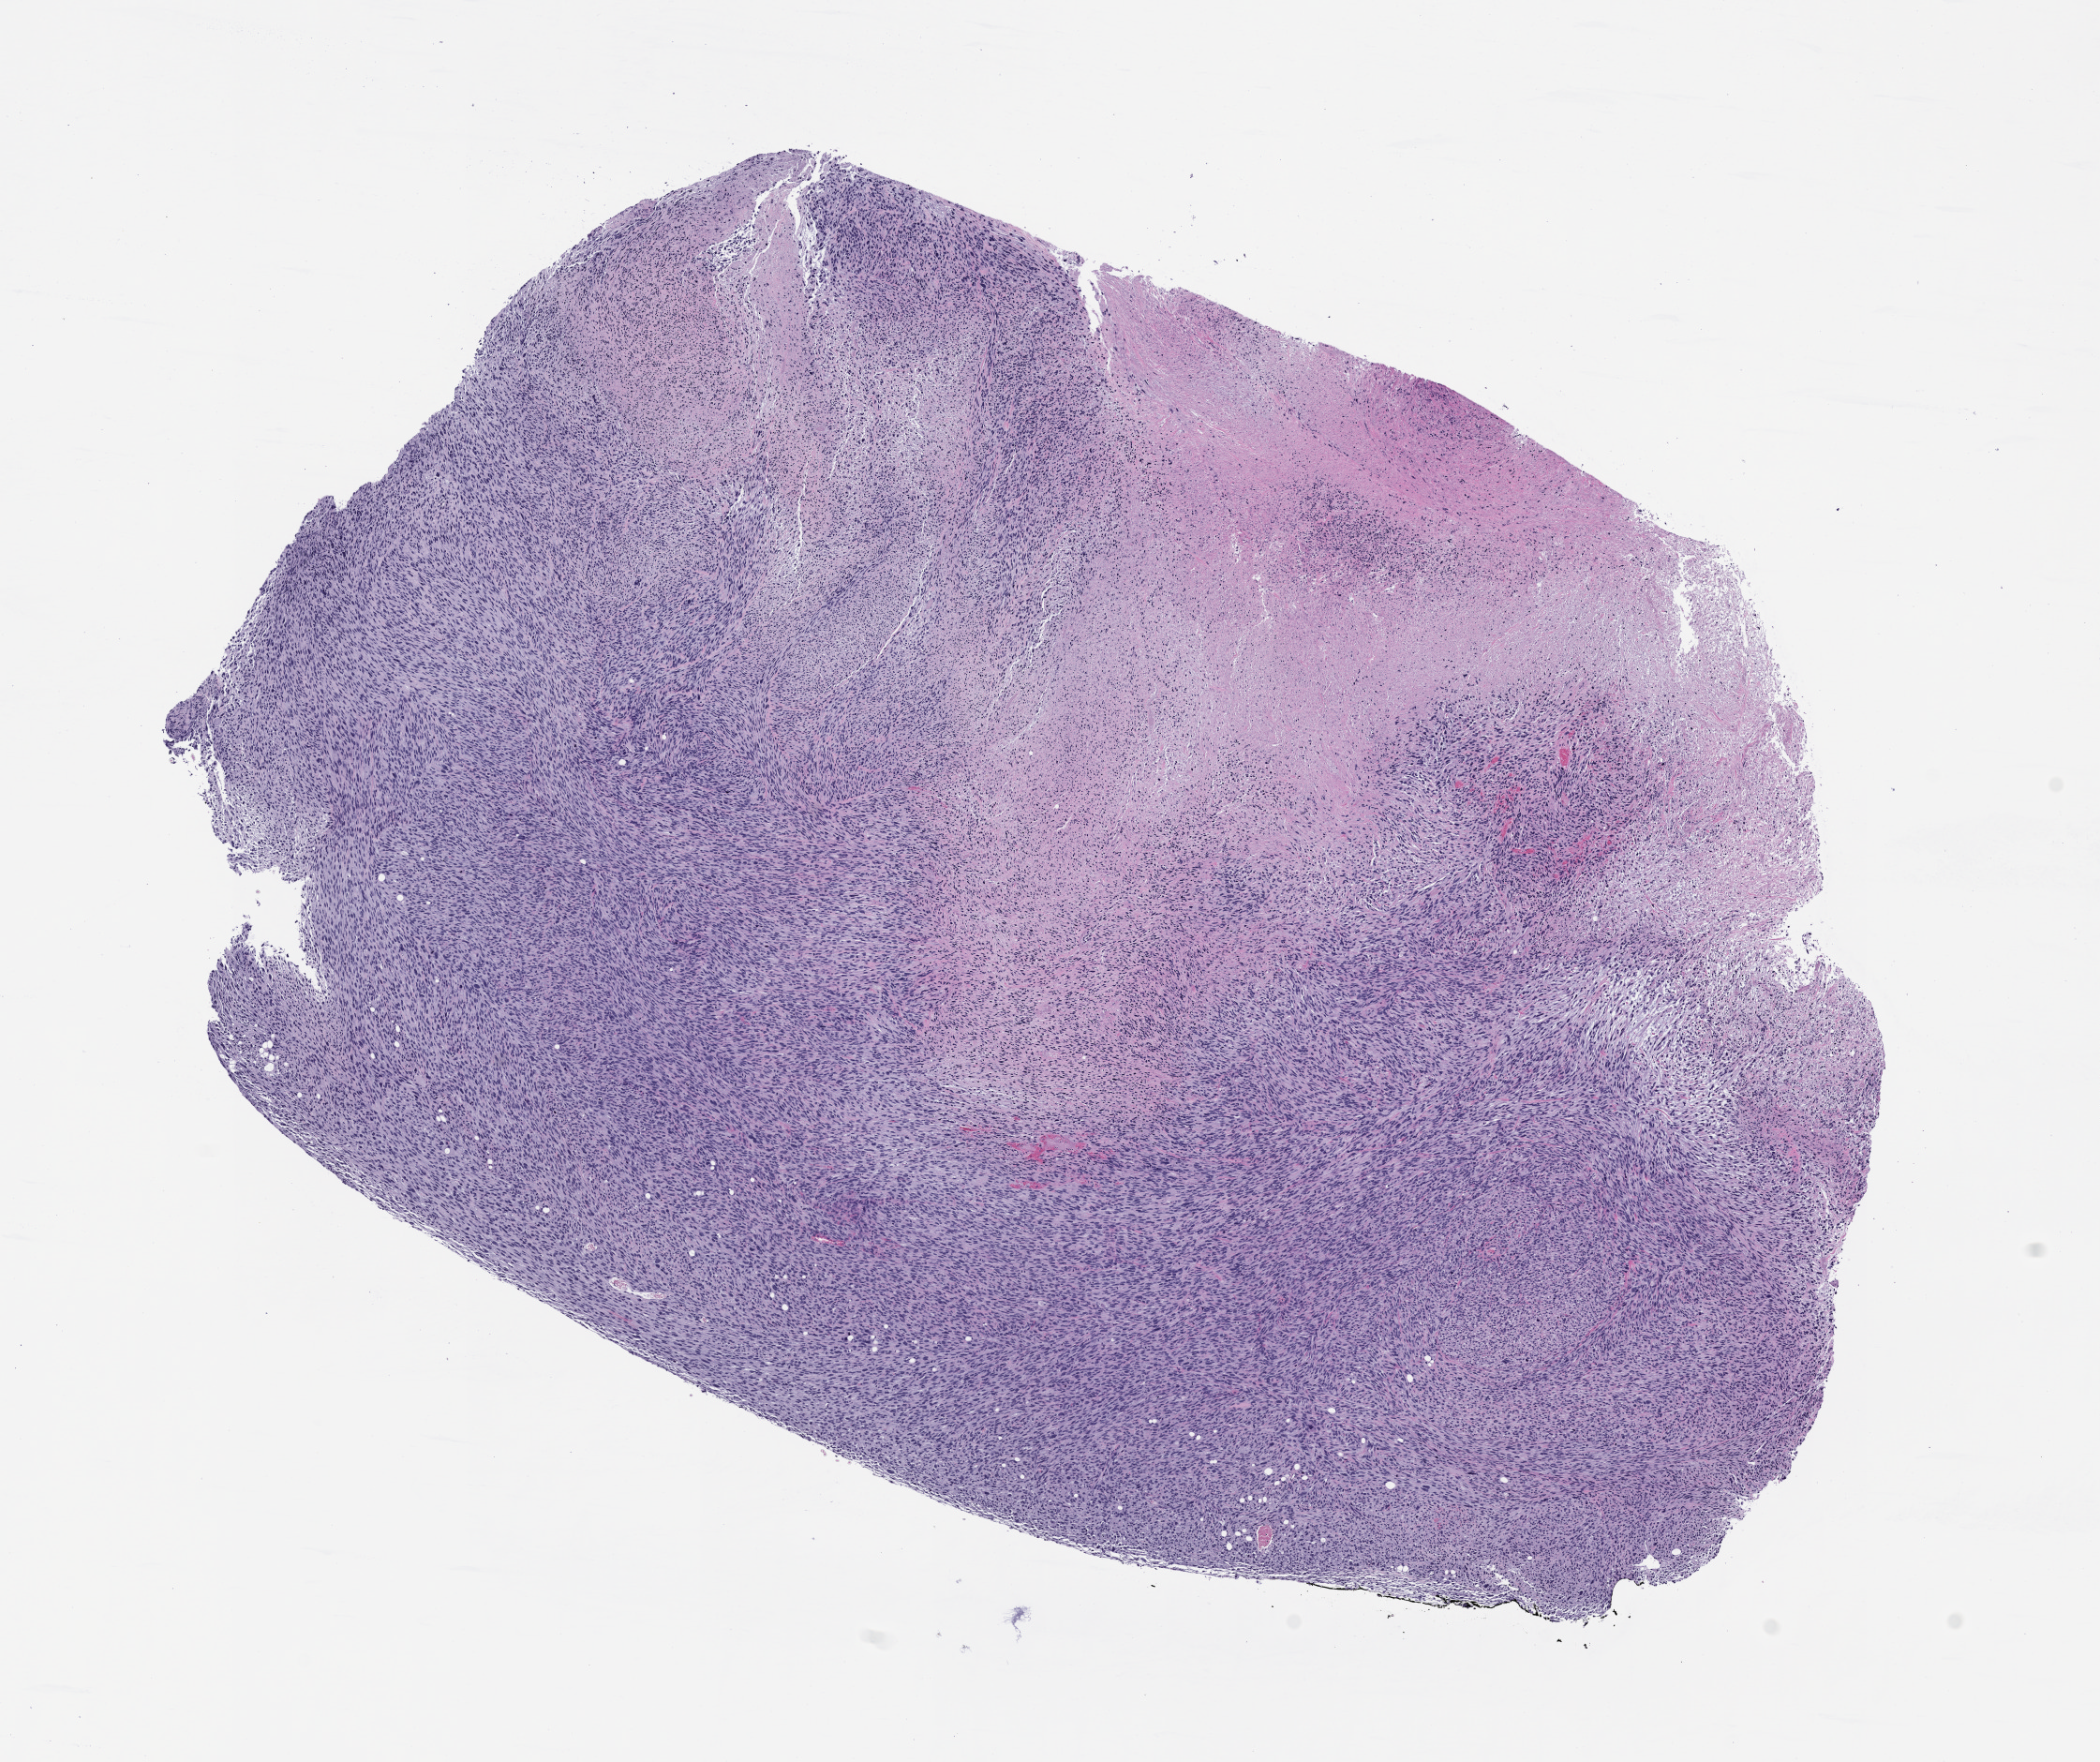
Whole-slide image, H&E: patient-derived xenograft (human tumor grown in a mouse), passage 1, whole scanned area (about 9.0 x 7.6 mm) shown as a low-resolution overview. Formalin-fixed paraffin-embedded section. Originating tumor site category: musculoskeletal.
* originating patient diagnosis: Non-Rhabdo. soft tissue sarcoma